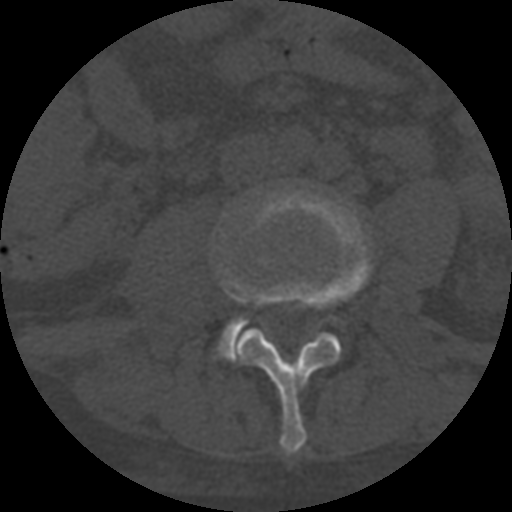
CT including the spine, one axial slice; slice 224 of 708 in the series (ordered by position); one of 3 acquisitions stored at this slice position; bone window (W 1800 / L 400 HU); 512 × 512 image matrix, field of view 160 × 160 mm. Patient age 55 years. Case-level facts recorded for this patient, not image findings: primary cancer: colon; vertebrae with lytic lesions (as recorded): T12, L1, L5.
Structures marked on this image (semi-automatically segmented with operator editing):
- L3 vertebra: box from (x=218, y=190) to (x=372, y=455) px
- L4 vertebra: (x=219, y=318)–(x=246, y=359)